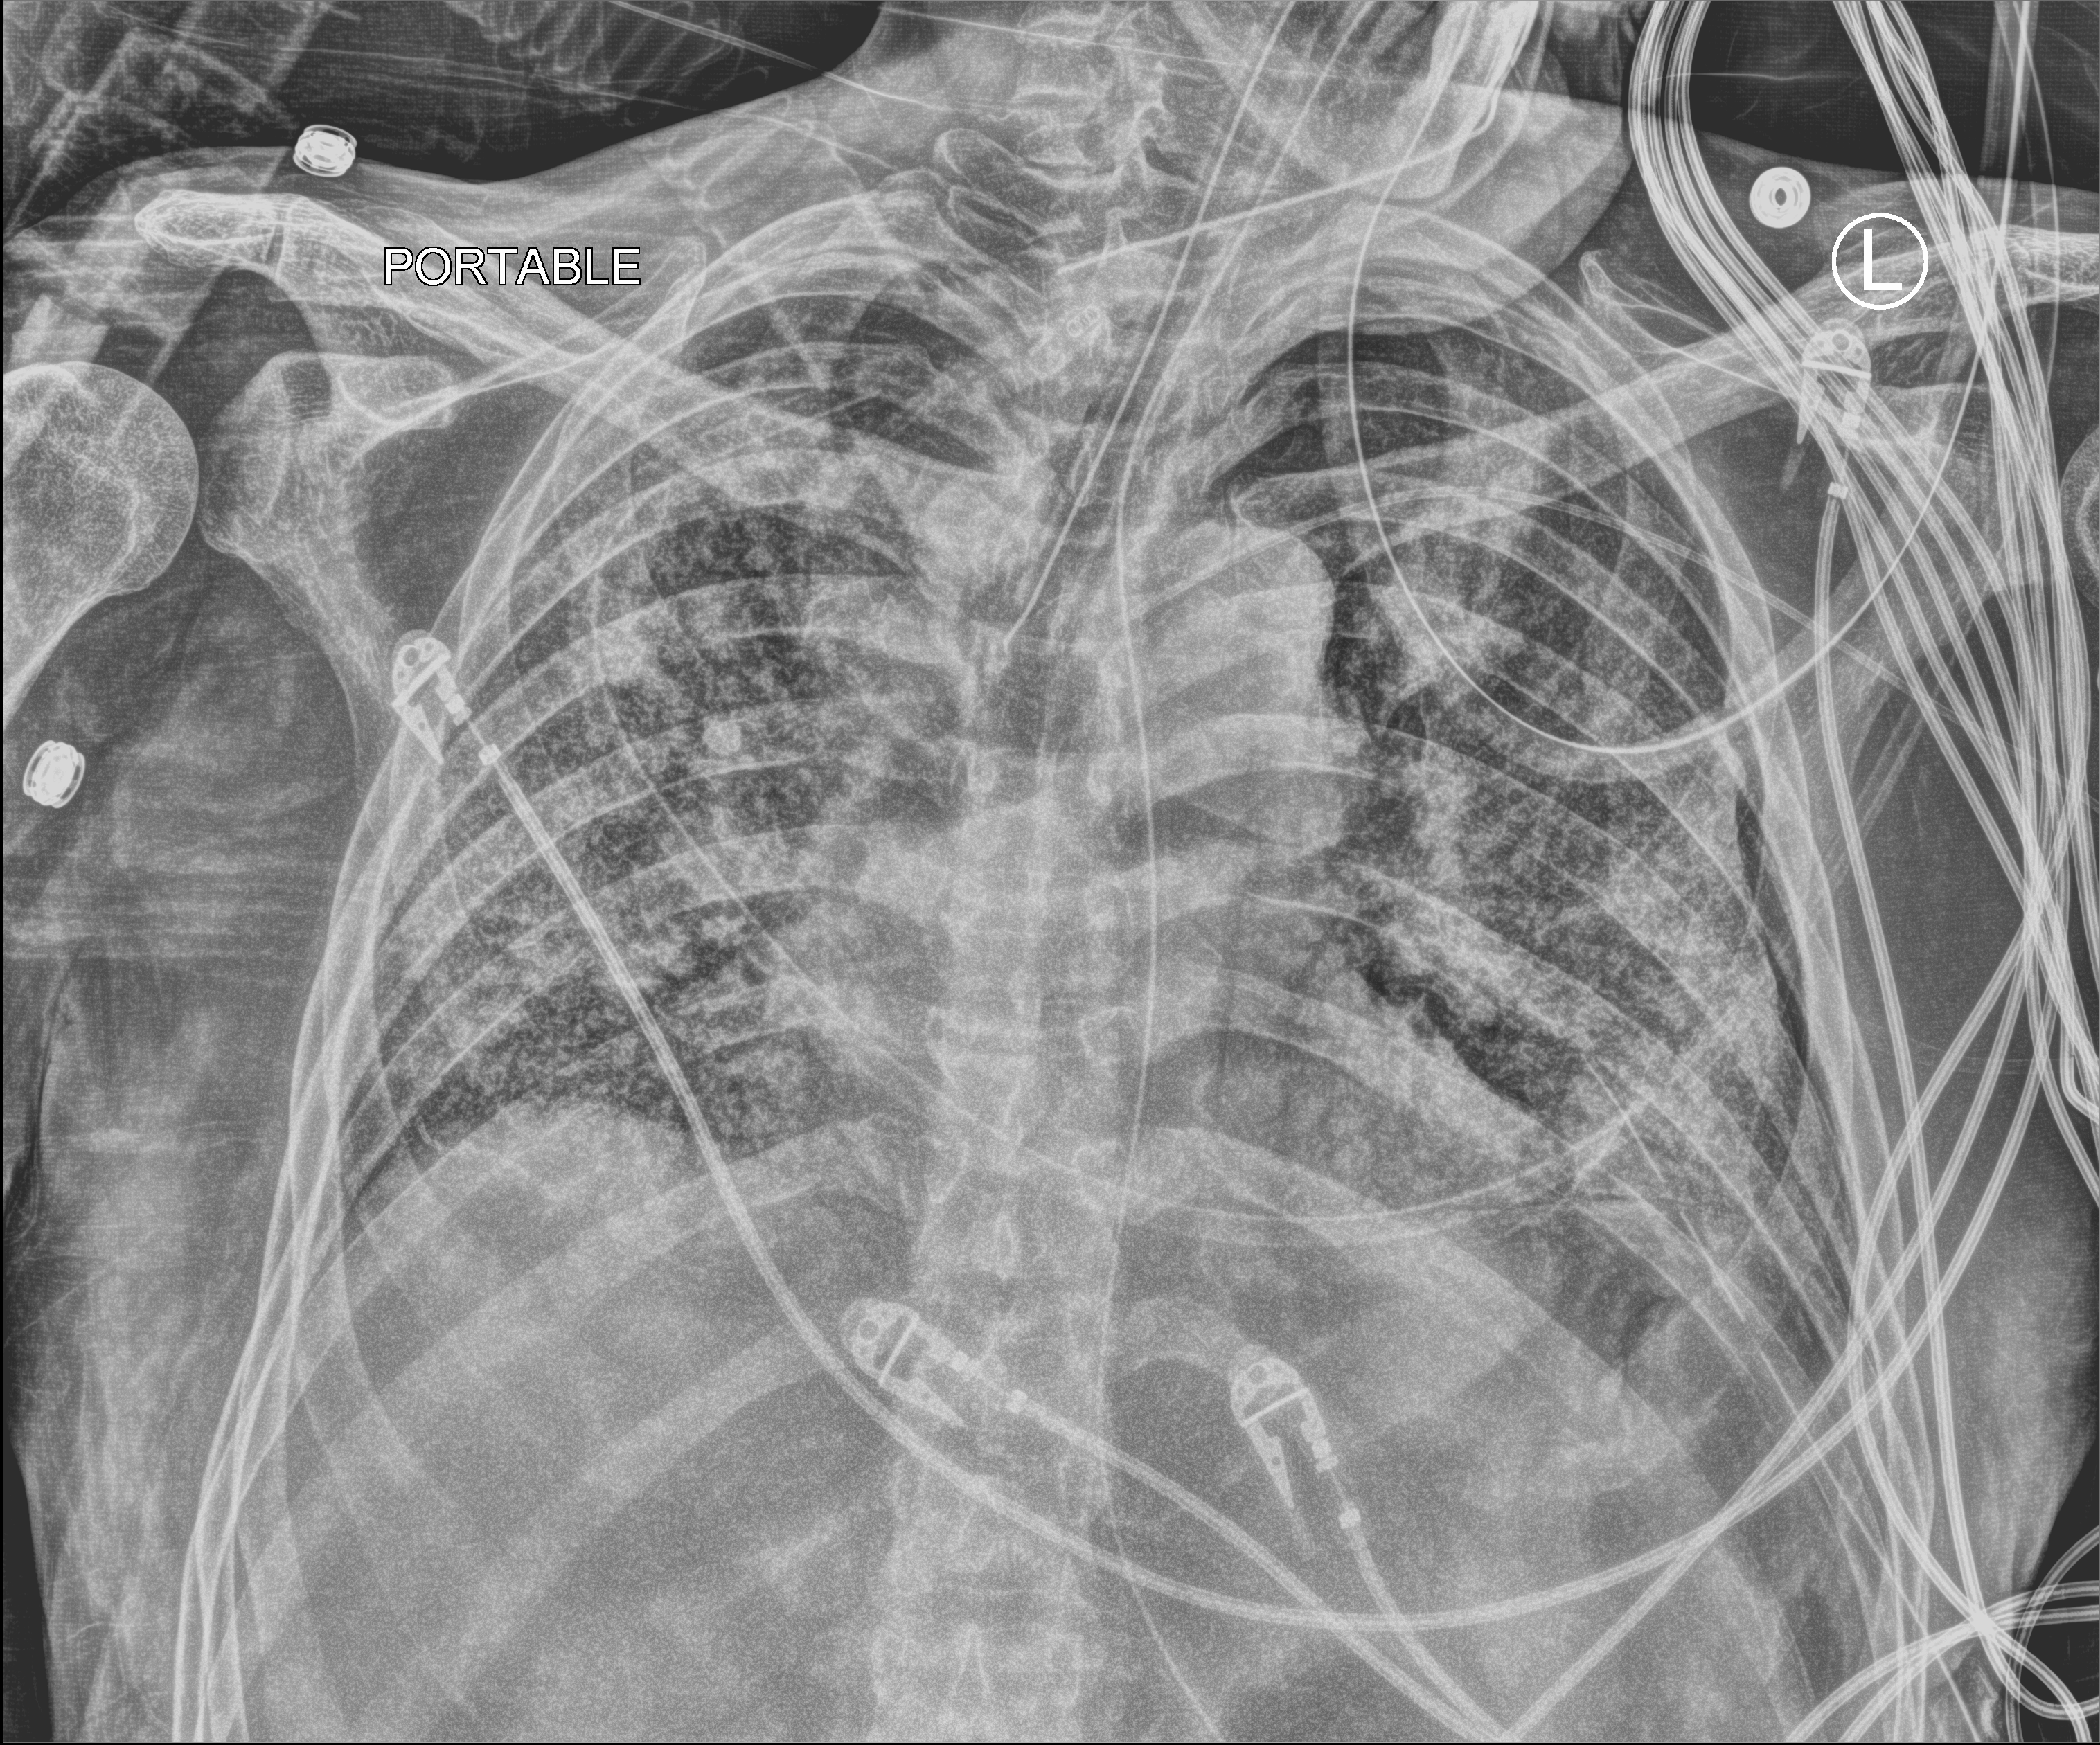
Bedside chest radiograph (computed radiography); anteroposterior (AP) projection. Patient hospitalised with COVID-19; male, aged 60–74 years.
Admission-level facts for this patient (not findings on this image; timing relative to this image not recorded):
- mechanically ventilated during this hospital stay: yes